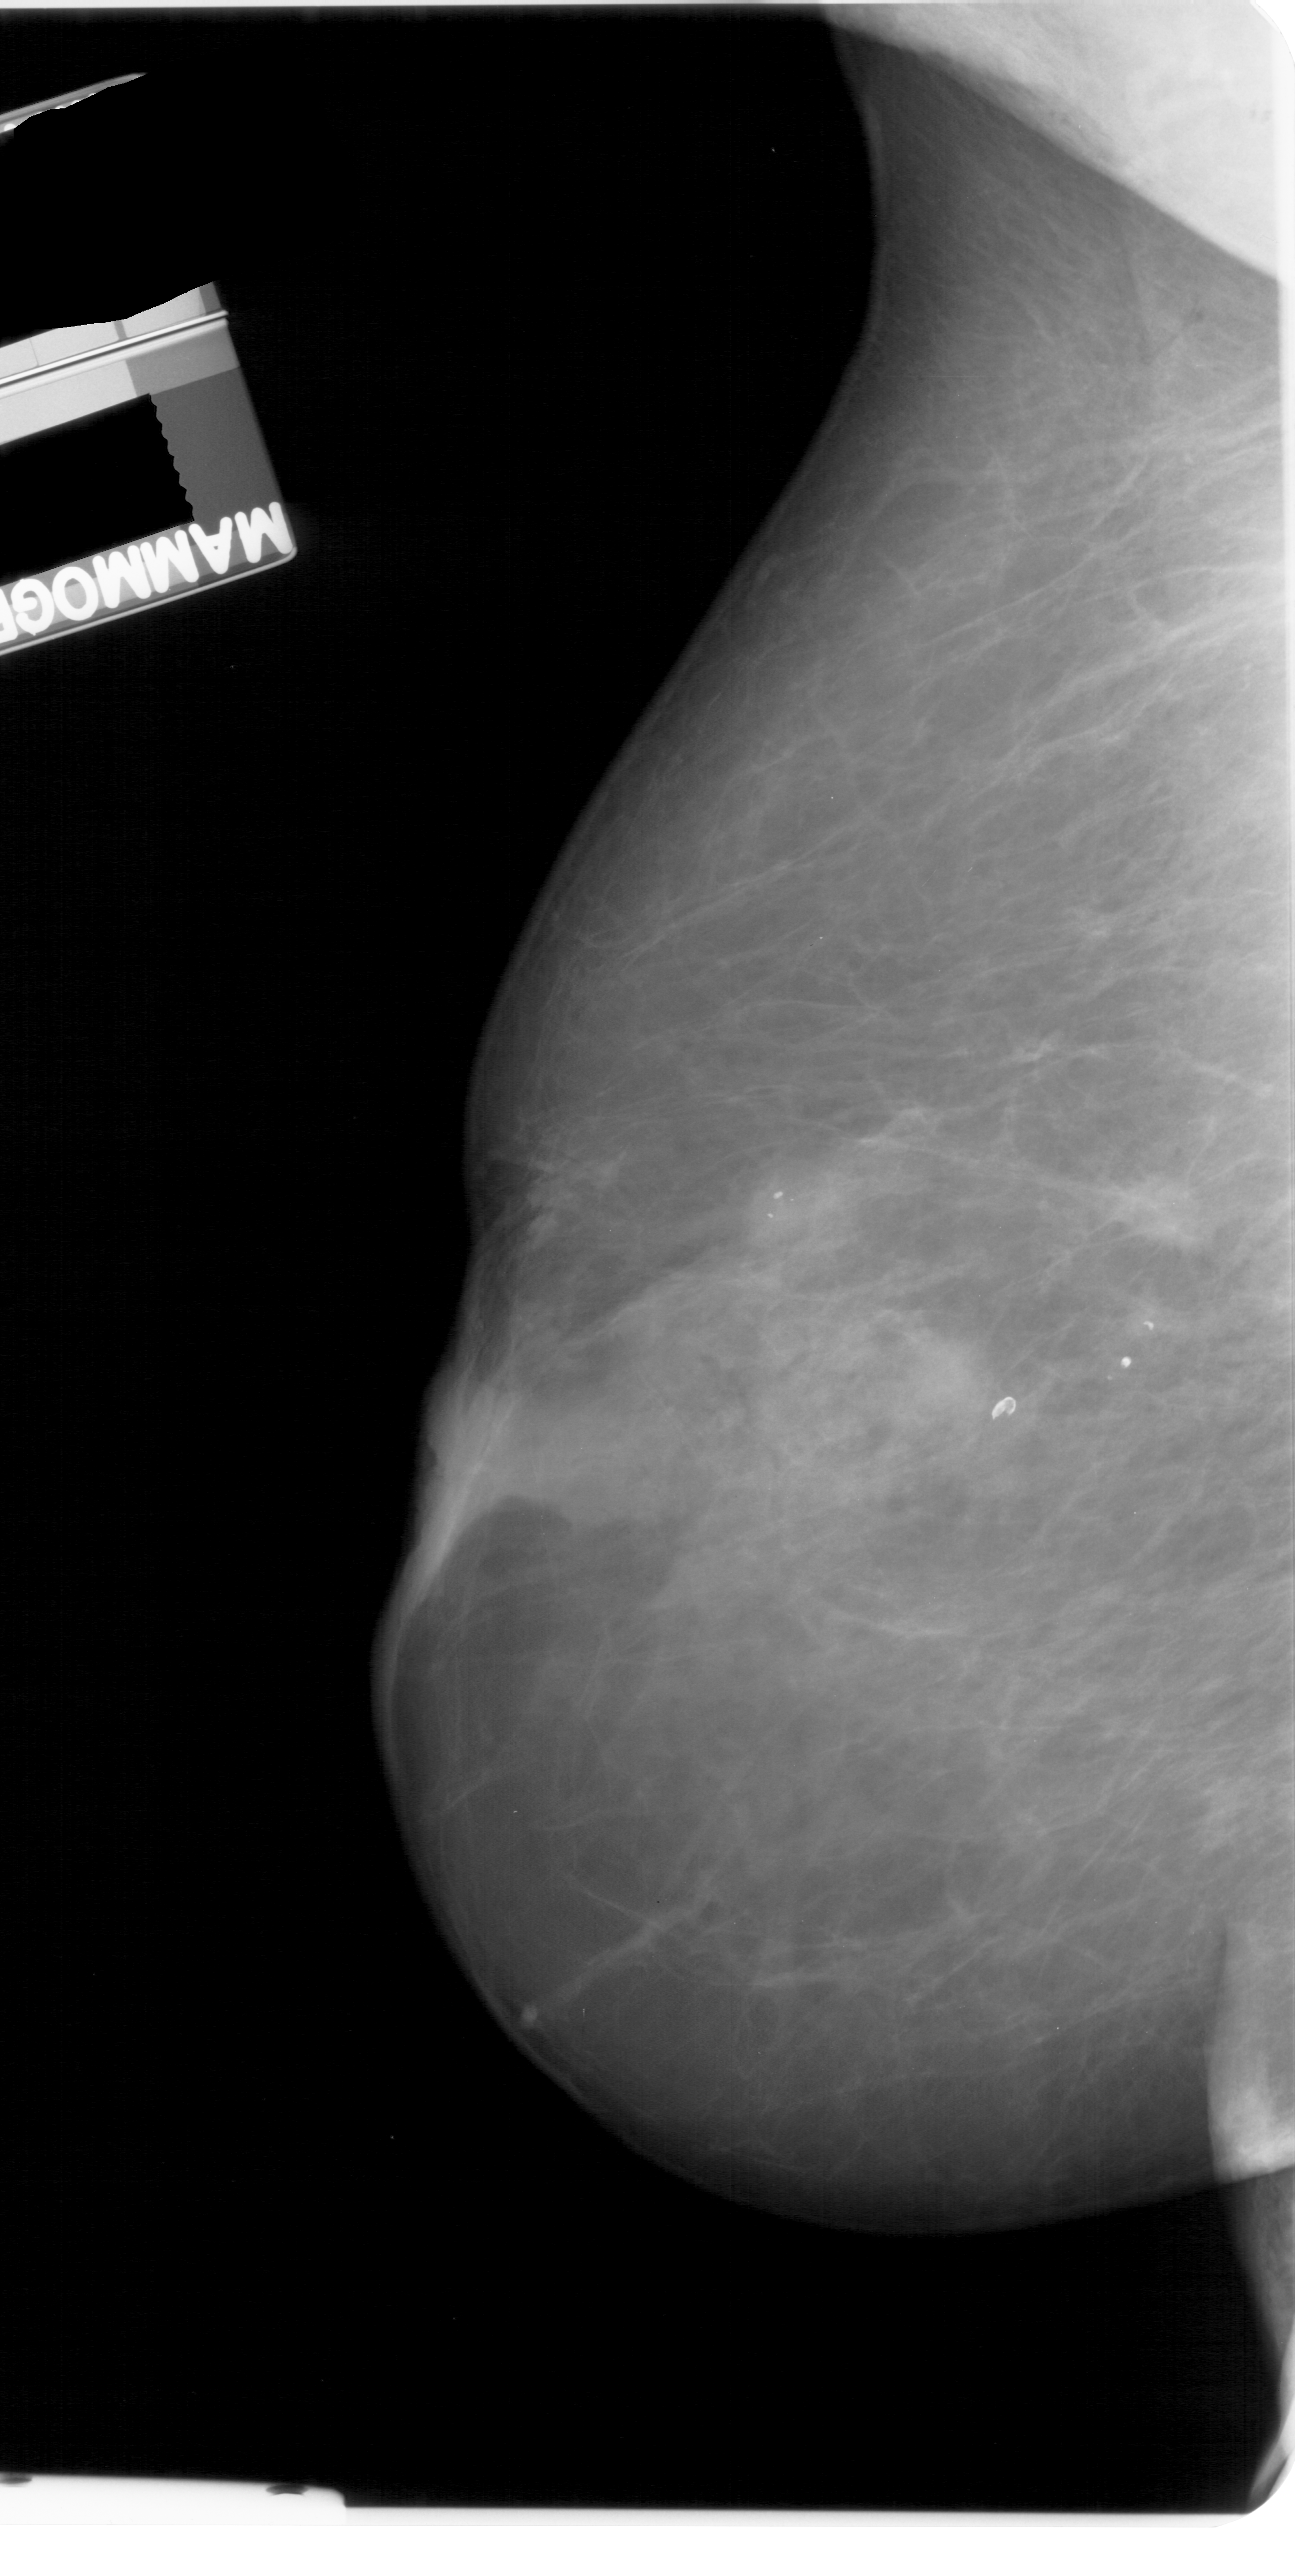
Digitized screen-film mammogram; left breast; mediolateral oblique (MLO) view; breast composition: extremely dense (BI-RADS density category 4 of 4).
Marked findings (only marked abnormalities are described; nothing is implied about the rest of the image): mass, shape oval, margins spiculated; BI-RADS assessment category 4; subtlety rating 3 on a 1 (subtle) to 5 (obvious) scale; pathology (as recorded): malignant.